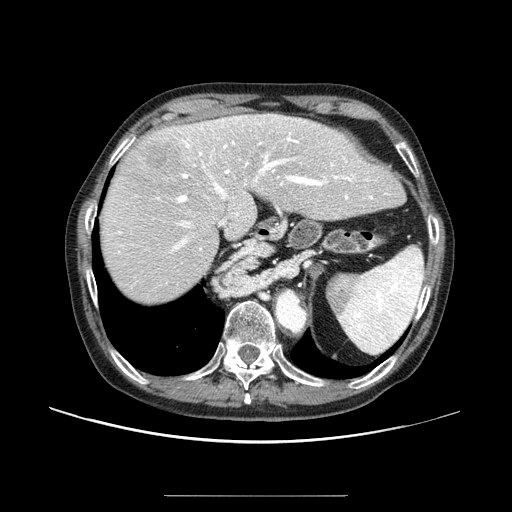
Contrast-enhanced abdominal CT (liver protocol), one axial slice; position 67 of 91 along the scan axis; reconstruction kernel STANDARD; 100 kVp; one of 2 acquisitions stored at this slice position; soft-tissue window (W 400 / L 40 HU); 512 × 512 image matrix, field of view 400 × 400 mm. Case-level facts recorded for this patient, not image findings: diagnosis: hepatocellular carcinoma (patient treated with transarterial chemoembolisation; whether this scan precedes or follows treatment is not stated here); TNM stage (as recorded): Stage-I; Child-Pugh class: A; tumour differentiation: moderately differentiated.
Structures marked on this image (semi-automatically segmented with operator editing):
- liver parenchyma outside the tumour (the mass and vessels are separate outlines, so this box may not span the whole liver): bounding box [x1, y1, x2, y2] px = [100, 114, 398, 302]
- mass: [138, 131, 186, 179]
- liver vessels: [118, 116, 373, 253]